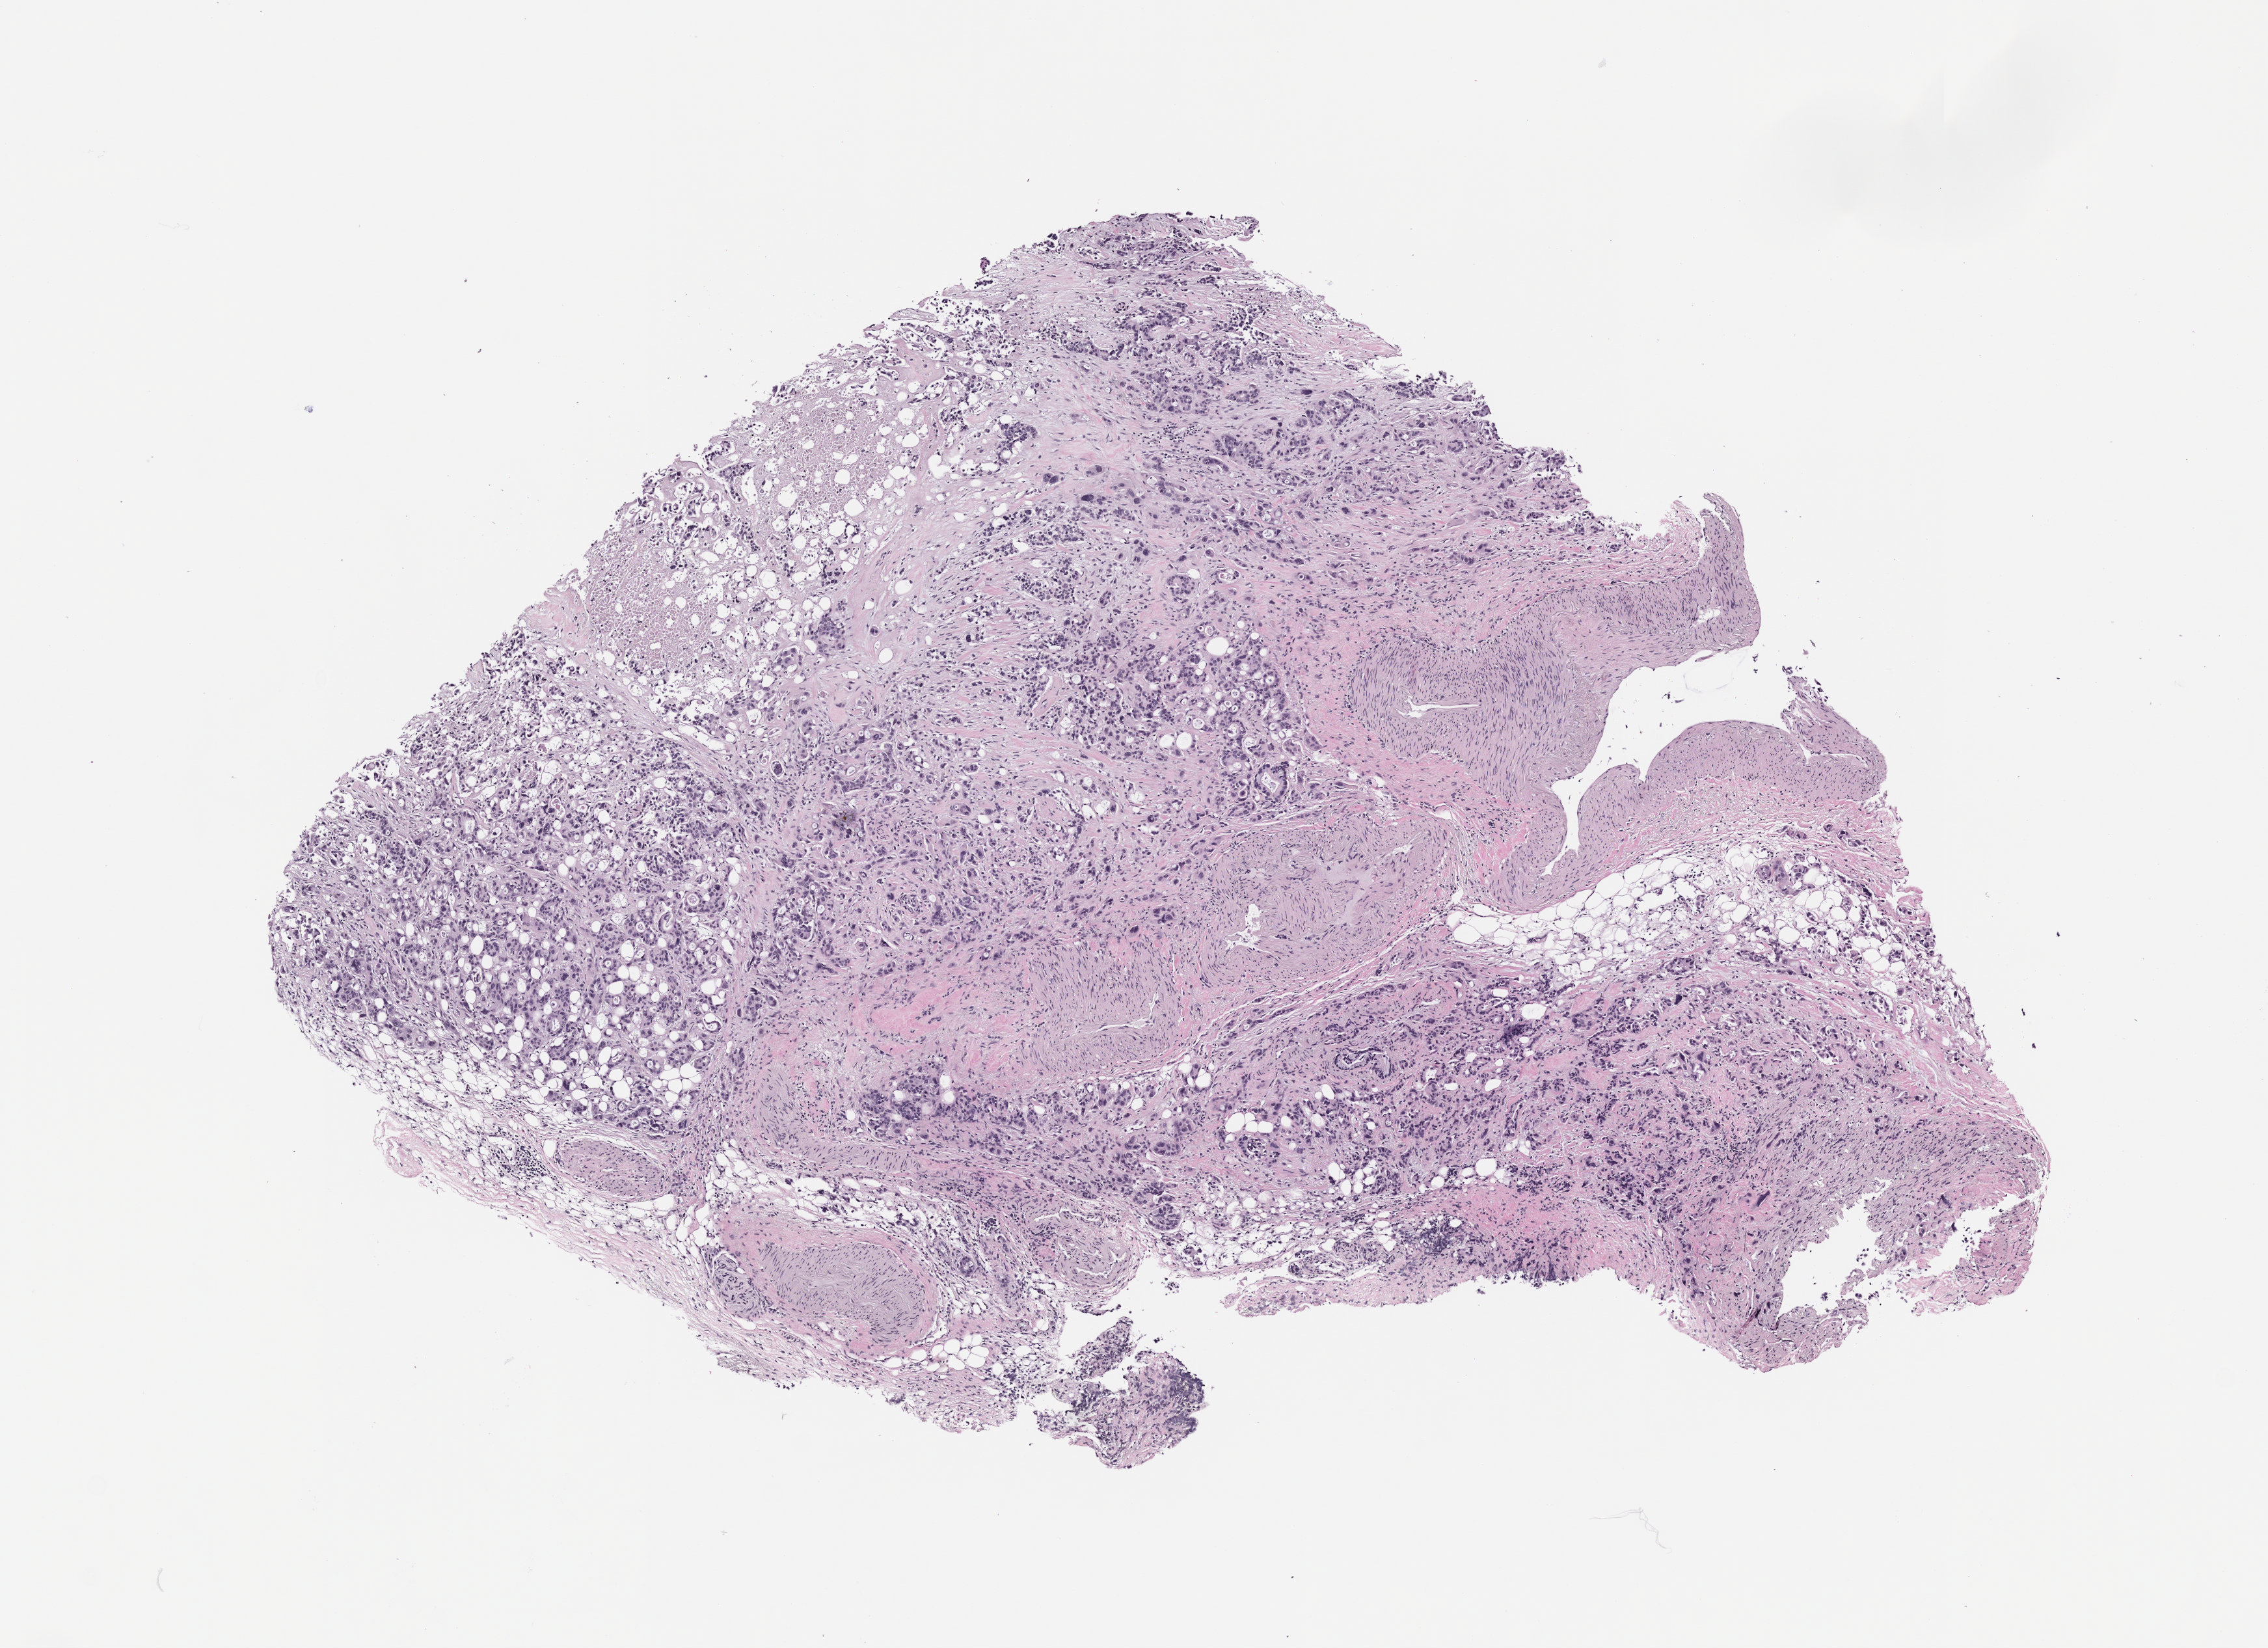
Digitized haematoxylin and eosin-stained section of the patient's (originator) tumor tissue, whole scanned area (about 7.0 x 5.1 mm) shown as a low-resolution overview; formalin-fixed, paraffin-embedded (FFPE) tissue; originating tumor site category: pancreas. Patient: female, age 62 years.
Diagnosis: Pancreatic Adenocarcinoma.